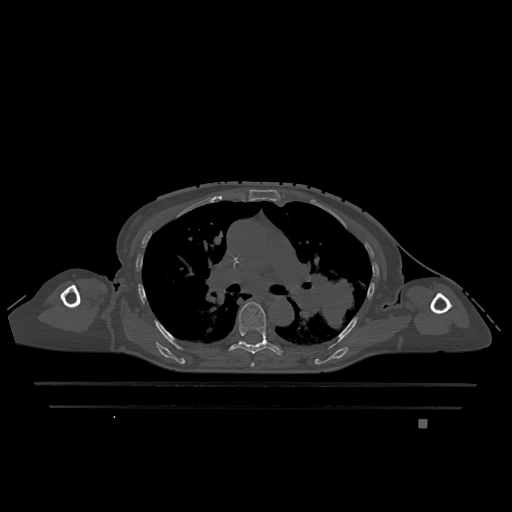
CT including the spine, one axial slice. Bone window (W 1800 / L 400 HU). 512 × 512 image matrix, field of view 500 × 500 mm. Patient: female, 74 years. Case-level facts recorded for this patient, not image findings: primary cancer: lung; vertebrae with lytic lesions (as recorded): T1, T4, T5, T6, L4, L5.
Outlined on this slice (semi-automatically segmented with operator editing):
- T5 vertebra: bounding box (x1, y1, x2, y2) in pixels: (251, 362, 255, 367)
- T6 vertebra: (229, 302, 283, 355)